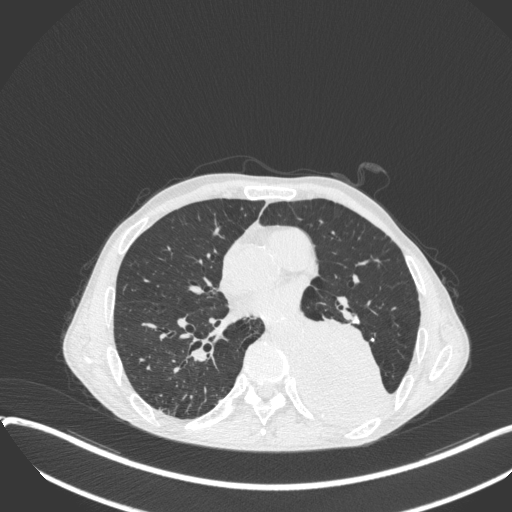
Chest CT, one axial slice; slice 171 of 400 in the series (ordered by position); lung window (W 1500 / L -600 HU); 1 mm slice thickness; 512 × 512 image matrix. Patient: male, 57 years. Case-level facts recorded for this patient, not image findings: clinical TNM (as recorded): T4 N0 M0.
Structures marked on this image (bounding box drawn by a radiologist):
- lung tumour (recorded histology: squamous cell carcinoma): bounding box <300,306,390,430> (left, top, right, bottom; pixels)